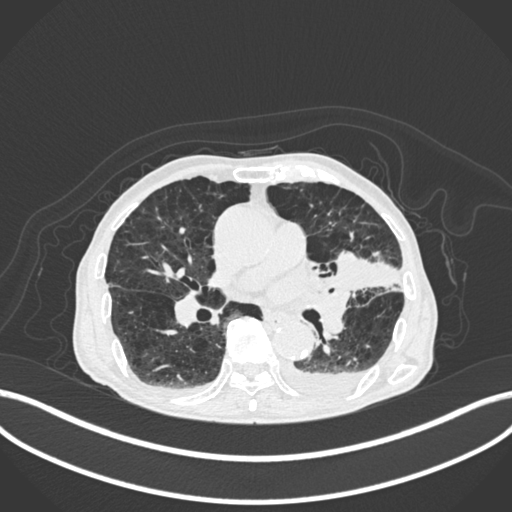
Chest CT, one axial slice. Position 112 of 400 along the scan axis. Reconstruction kernel B30f. Lung window (W 1500 / L -600 HU). 1 mm slice thickness. 512 × 512 image matrix. Patient: male, 90 years or older. From the clinical record (not read from this slice): clinical TNM (as recorded): T2b N1 M0.
Outlined on this slice (bounding box drawn by a radiologist):
- lung tumour (recorded histology: squamous cell carcinoma): bounding box <330,243,406,292> (left, top, right, bottom; pixels)